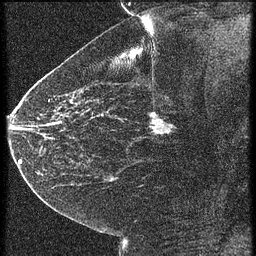
Breast MRI (dynamic contrast-enhanced), one sagittal slice; slice 35 of 60 in the series (ordered by position); 4 images stored at this slice position (order not interpretable as contrast timing); 1.5 T; TE 4.2 ms, TR 21.3 ms; 1.5 mm slice thickness; 256 × 256 image matrix, field of view 180 × 180 mm. Patient: female, 43 years. From the clinical record (not read from this slice): setting: breast cancer imaged before/during neoadjuvant chemotherapy; receptor status: HER2-positive.
Structures marked on this image (semi-automatic segmentation, software-assisted and operator-edited):
- analysis volume of interest (the breast-tissue region the enhancement analysis was run in; not a lesion): bounding box [x1, y1, x2, y2] px = [122, 100, 187, 151]
- tumour enhancement mask (voxels above the 90 % enhancement threshold inside the analysis volume of interest): [150, 112, 173, 135]